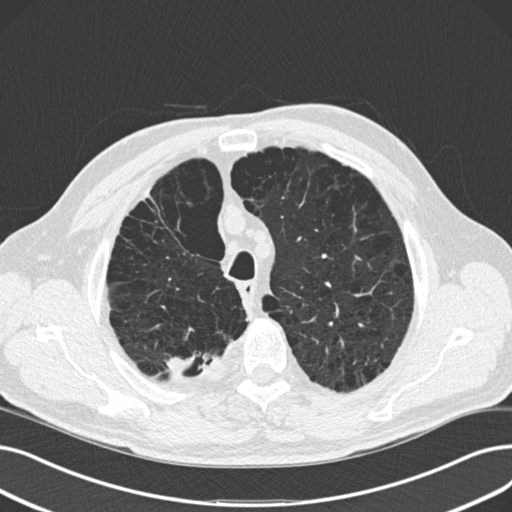
Low-dose screening chest CT, one axial slice. Position 125 of 165 along the scan axis. Reconstruction kernel B30f. Lung window (W 1500 / L -600 HU). 2 mm slice thickness. 512 × 512 image matrix, field of view 369 × 369 mm.
Annotated regions visible in this slice (manually delineated by an expert):
- lesion 2 (tumor, upper lobe of right lung): bounding box <166,357,186,374> (left, top, right, bottom; pixels)